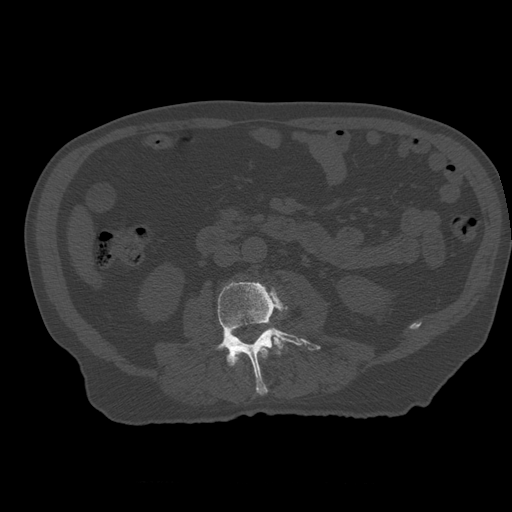
CT including the spine, one axial slice; position 189 of 399 along the scan axis; bone window (W 1800 / L 400 HU); 1.25 mm slice thickness; 512 × 512 image matrix, field of view 407 × 407 mm. Patient age 73 years. From the clinical record (not read from this slice): primary cancer: prostate; vertebrae with lytic lesions (as recorded): L2.
Outlined on this slice (semi-automatically segmented with operator editing):
- L2 vertebra: box from (x=231, y=345) to (x=269, y=367) px
- L3 vertebra: (x=214, y=282)–(x=320, y=394)
- L4 vertebra: (x=274, y=340)–(x=282, y=349)